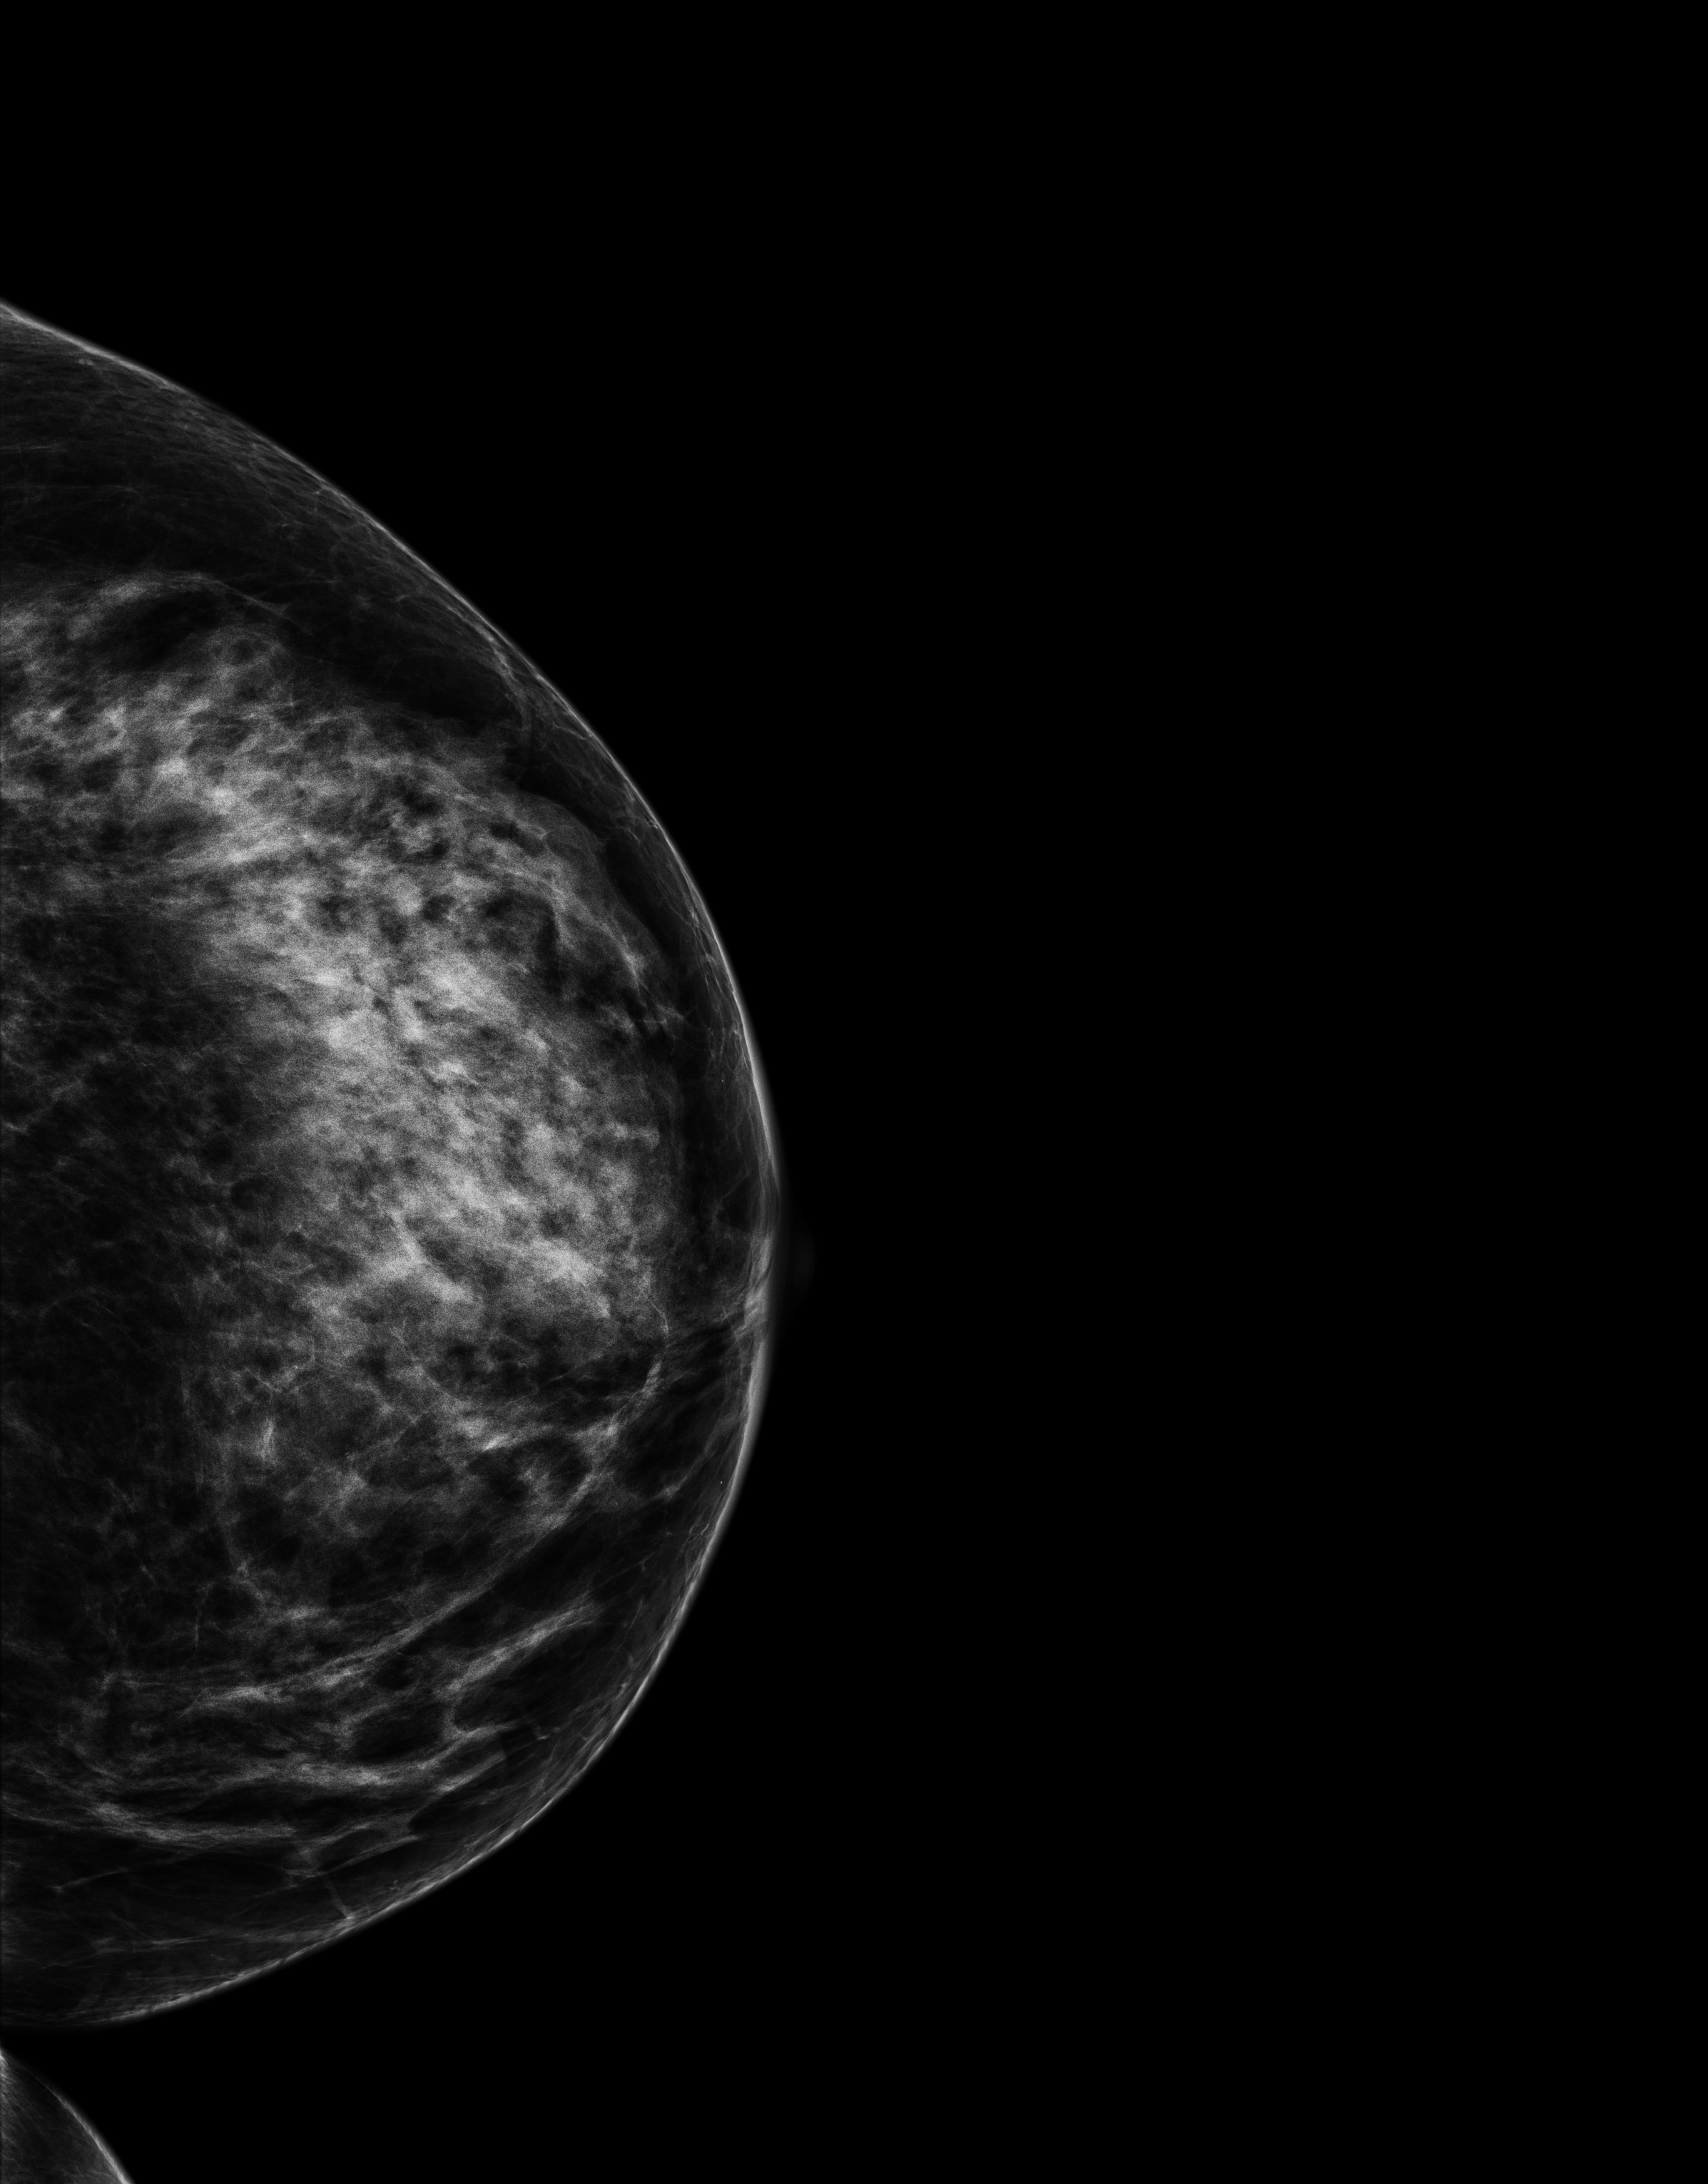
Screening examination. Patient aged 64 years (female).
Image type: full-field digital mammogram. Breast: left. Projection: craniocaudal (CC) view. BI-RADS breast density category at the screening exam (both breasts, scale 1–4): 4. Final BI-RADS category for the screening round (tomosynthesis exam, both breasts): category 2. Recall: no recall after this screen.